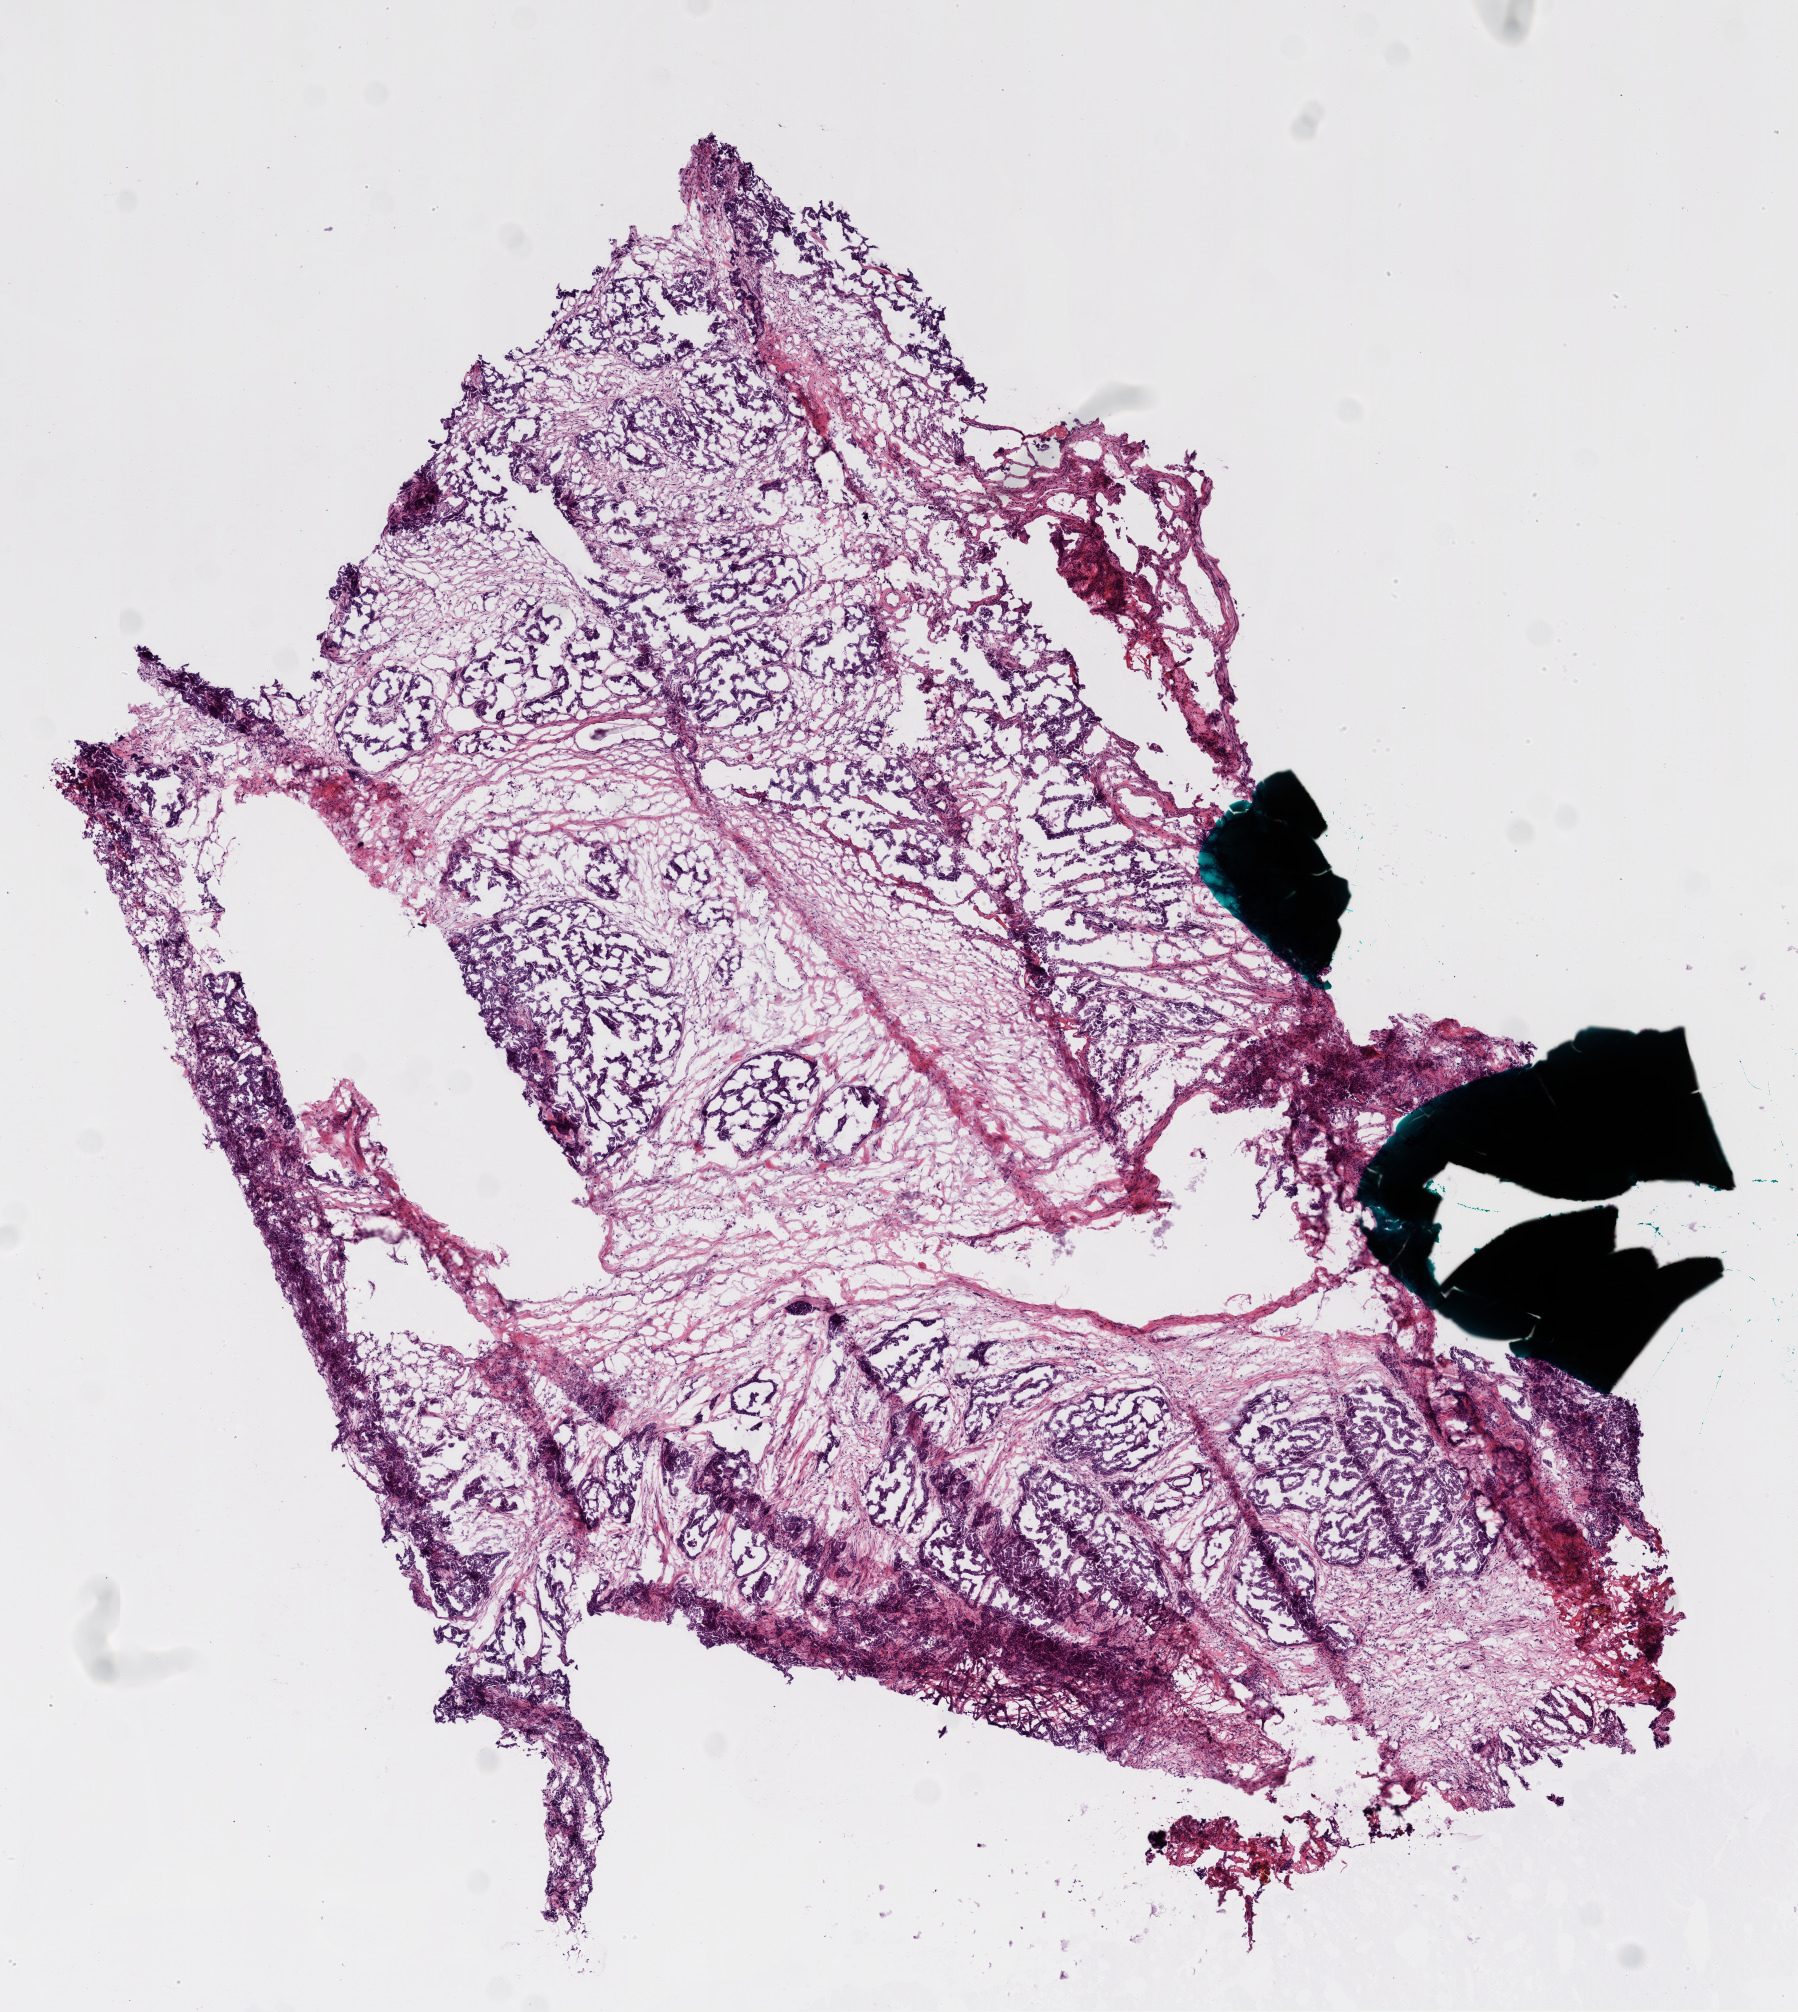
H&E whole-slide image, whole scanned area (about 7.3 x 8.1 mm) shown as a low-resolution overview; frozen section from the bottom of the tissue portion; sample: primary tumour, ovary. Patient: female, age at initial diagnosis 78 years.
Diagnosis: Serous cystadenocarcinoma, NOS.